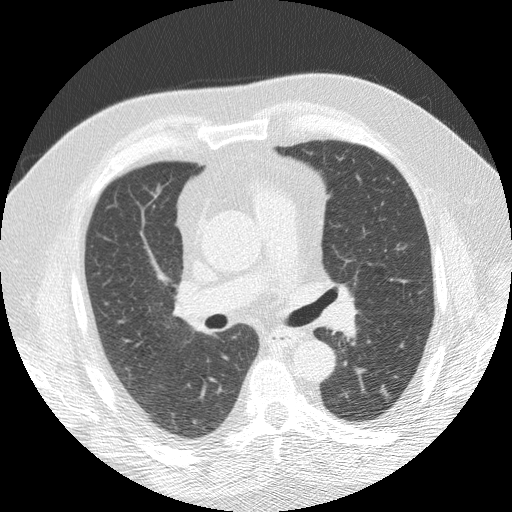
Low-dose screening chest CT, axial slice, first (baseline) screen, lung window (W 1500 / L -600 HU), standard (soft-tissue) reconstruction kernel (STANDARD), slice 67 of 166 in the series, 512 × 512 image matrix, field of view 360 × 360 mm. Male participant, aged 69 years at enrolment. Former smoker at enrolment.
Lesion marked by an expert reader, bounding box (x1, y1, x2, y2) in pixels: (366, 376, 401, 414). Screening reader's record for this exam: no non-calcified nodule ≥4 mm recorded. Participant outcome: lung cancer diagnosed 939 days after this screen (after the third annual screen) — squamous cell carcinoma, NOS, left lower lobe, moderately differentiated (G2), stage IA (AJCC 6th edition), 14 mm at pathology.